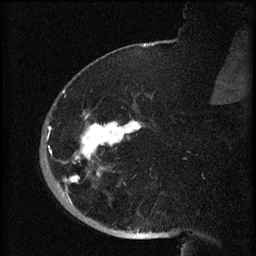
Breast MRI (dynamic contrast-enhanced), one sagittal slice. Position 17 of 60 along the scan axis. Dynamic contrast-enhanced series, image 2 of 3 at this slice position (ordered by acquisition). 1.5 T. TE 4.2 ms, TR 8.2 ms. 2 mm slice thickness. 256 × 256 image matrix, field of view 180 × 180 mm. Patient: female, 71 years.
Annotated regions visible in this slice (semi-automatically segmented with operator editing):
- analysis volume of interest (the breast-tissue region the enhancement analysis was run in; not a lesion): box from (x=40, y=72) to (x=144, y=196) px
- tumour enhancement mask (voxels above the 70 % enhancement threshold inside the analysis volume of interest): (x=47, y=90)–(x=141, y=196)